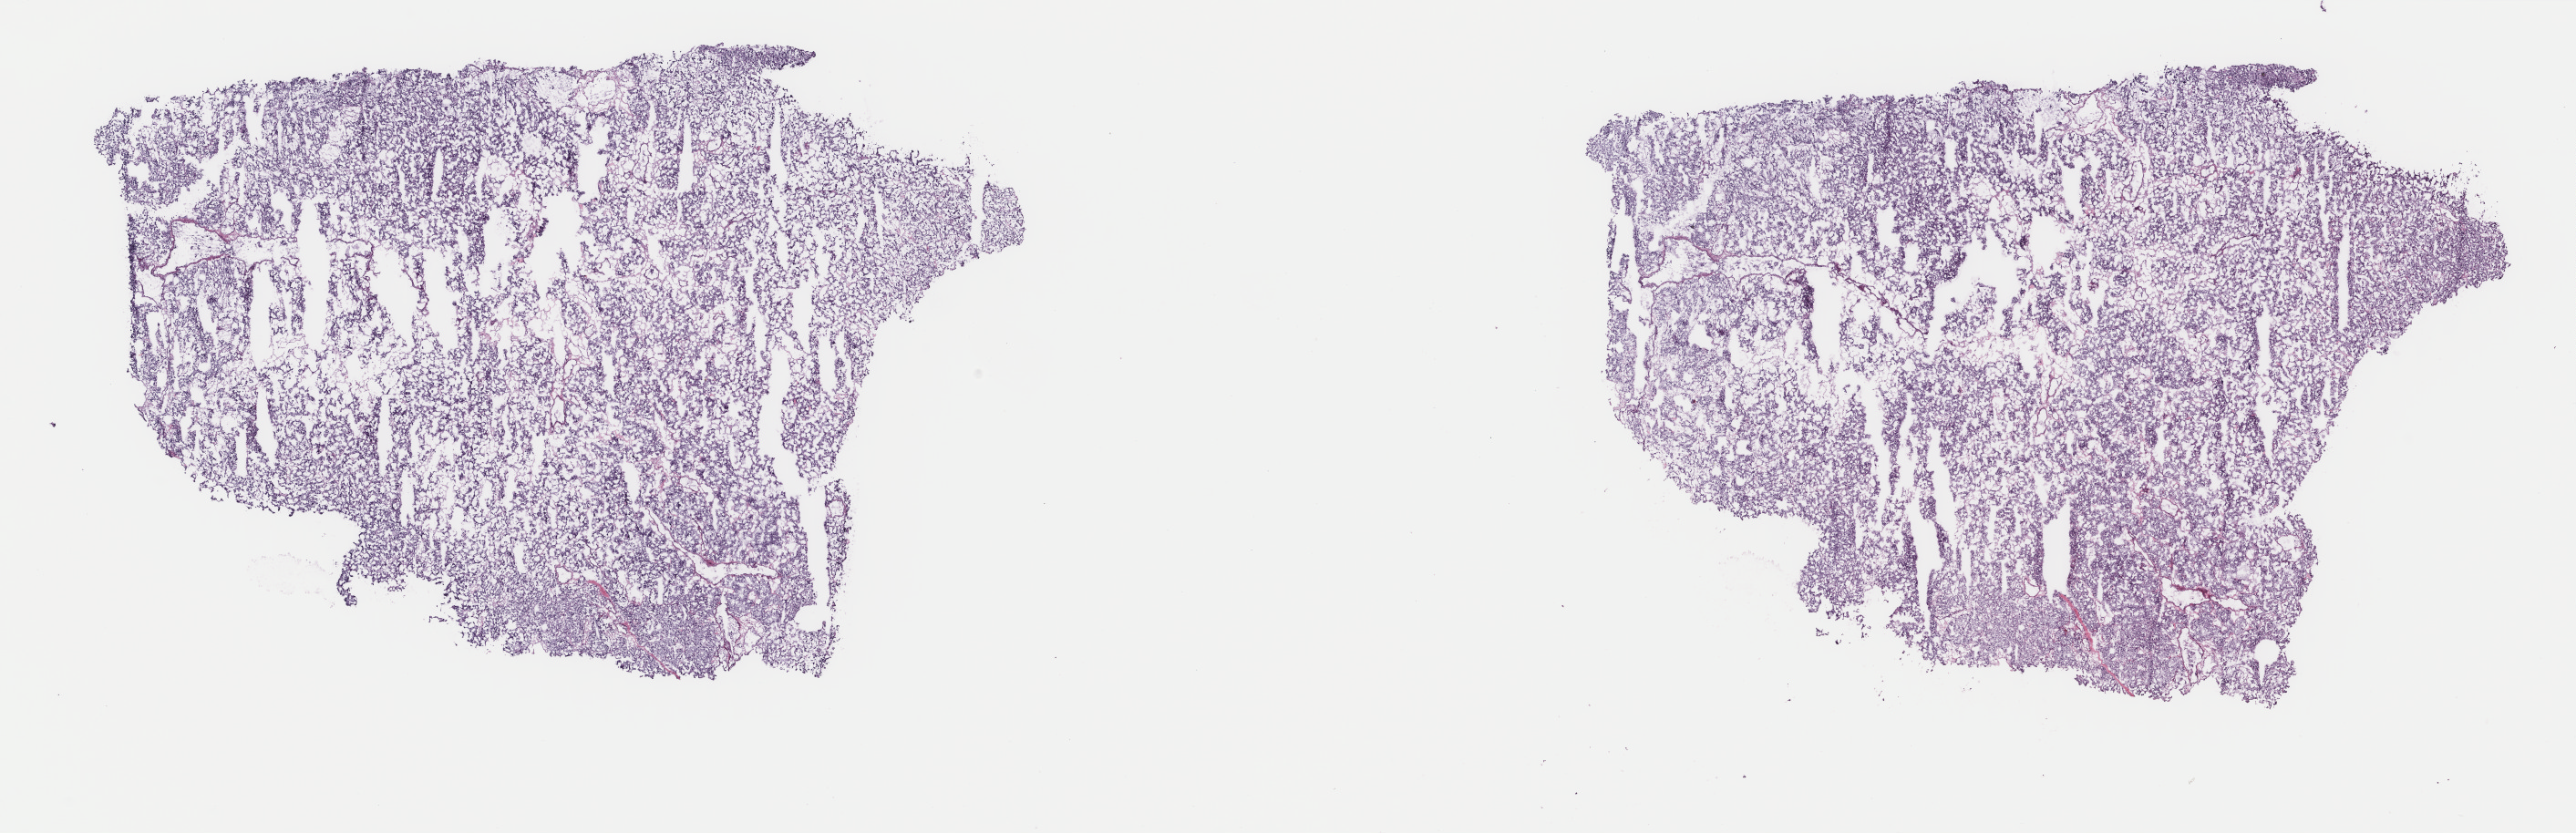
Whole-slide histology image, Hematoxylin and eosin (H&E) stained, whole scanned area (about 22.4 x 7.3 mm) shown as a low-resolution overview; frozen section from the top of the tissue portion; sample: primary tumour, adrenal gland. Female patient; age at initial diagnosis 51 years. Pathologist review of this section (percent, as recorded): tumour cells 85%, tumour nuclei 100%, normal cells 0%, stromal cells 15%, necrosis 0%. Infiltration values recorded for this section: lymphocyte infiltration 0%, monocyte infiltration 0%, neutrophil infiltration 0%.
- laterality: right
- histologic diagnosis: Pheochromocytoma, NOS